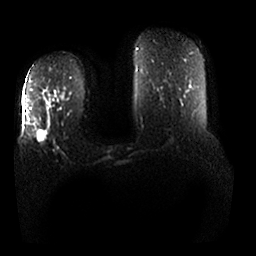
Breast MRI, one axial slice; position 12 of 25 along the scan axis; diffusion-weighted series; image 2 of 4 stored at this slice position (different b-values; order by instance number); 1.5 T; 256 × 256 image matrix, field of view 380 × 380 mm. Female patient.
Structures marked on this image (outlined manually by an expert reader):
- tumour on diffusion-weighted imaging: bounding box <37,131,46,141> (left, top, right, bottom; pixels)